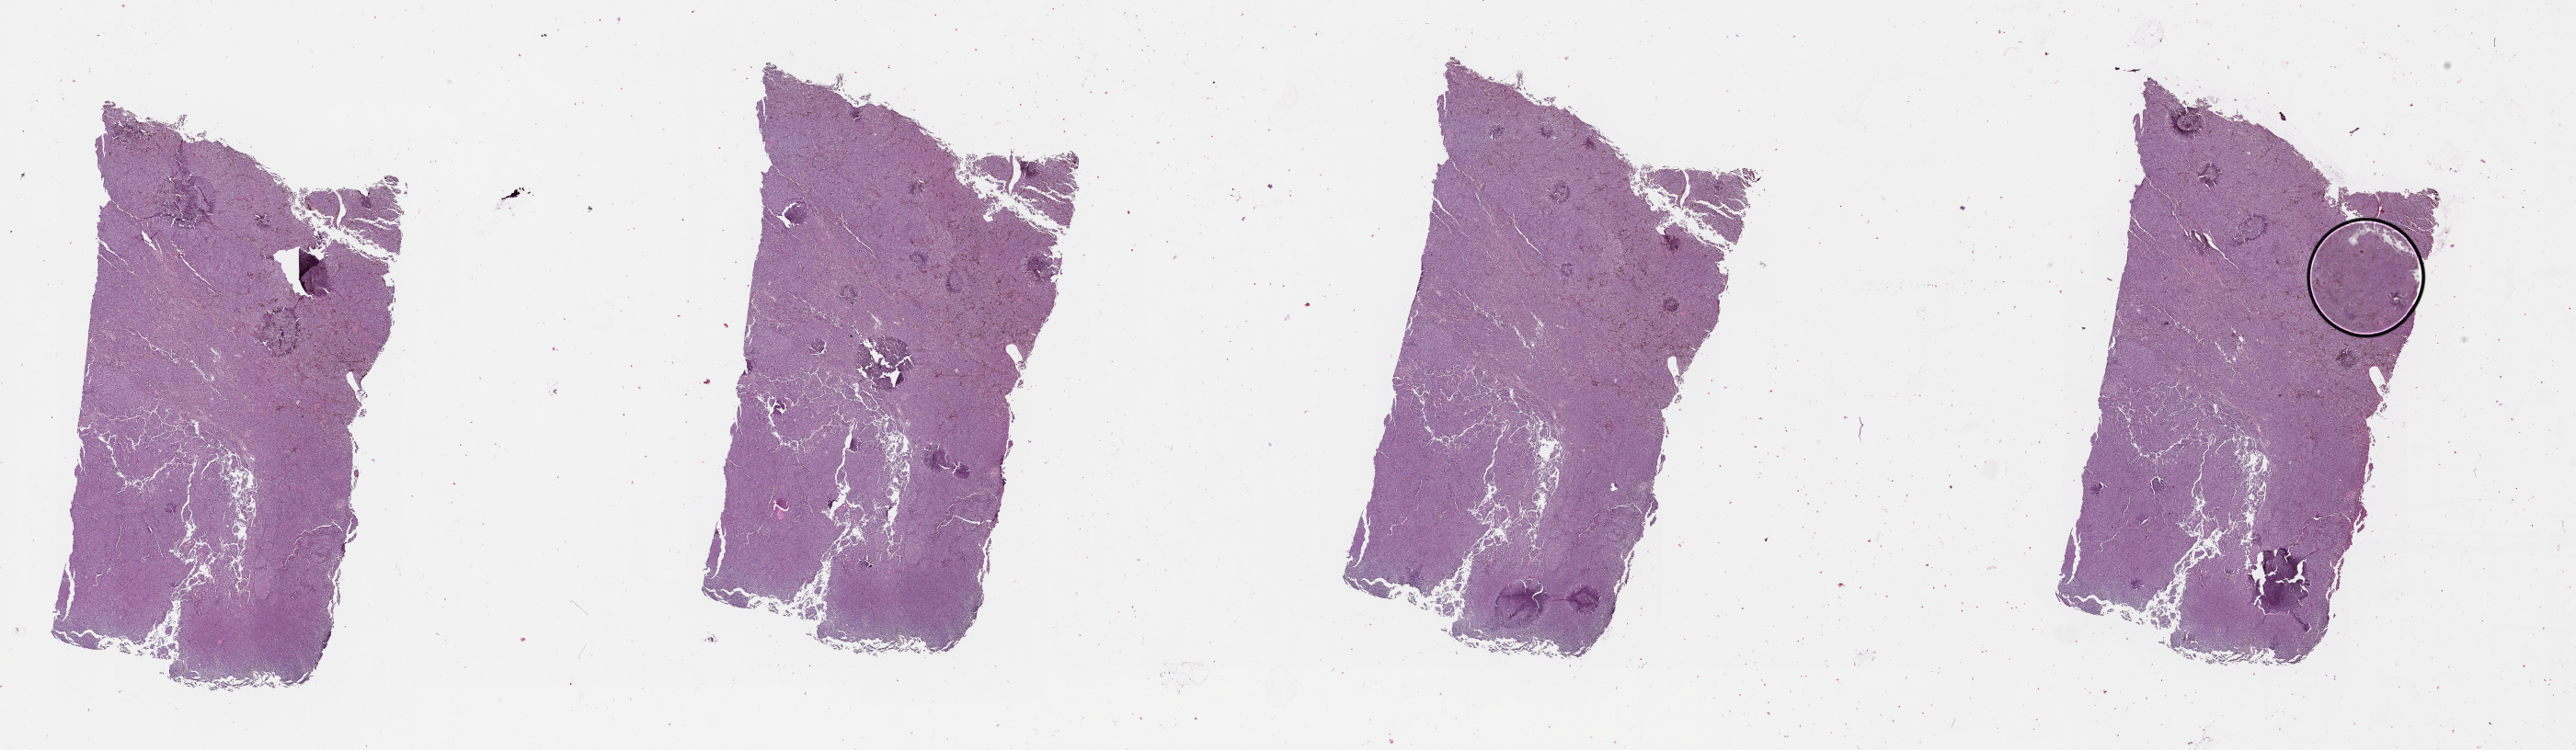
Digitized H&E tissue section (whole slide) — low-resolution overview of the scanned area, about 45.1 x 13.1 mm (slide scanned at 20x). 70-year-old female patient.
Patient diagnosis: Malignant melanoma, NOS.